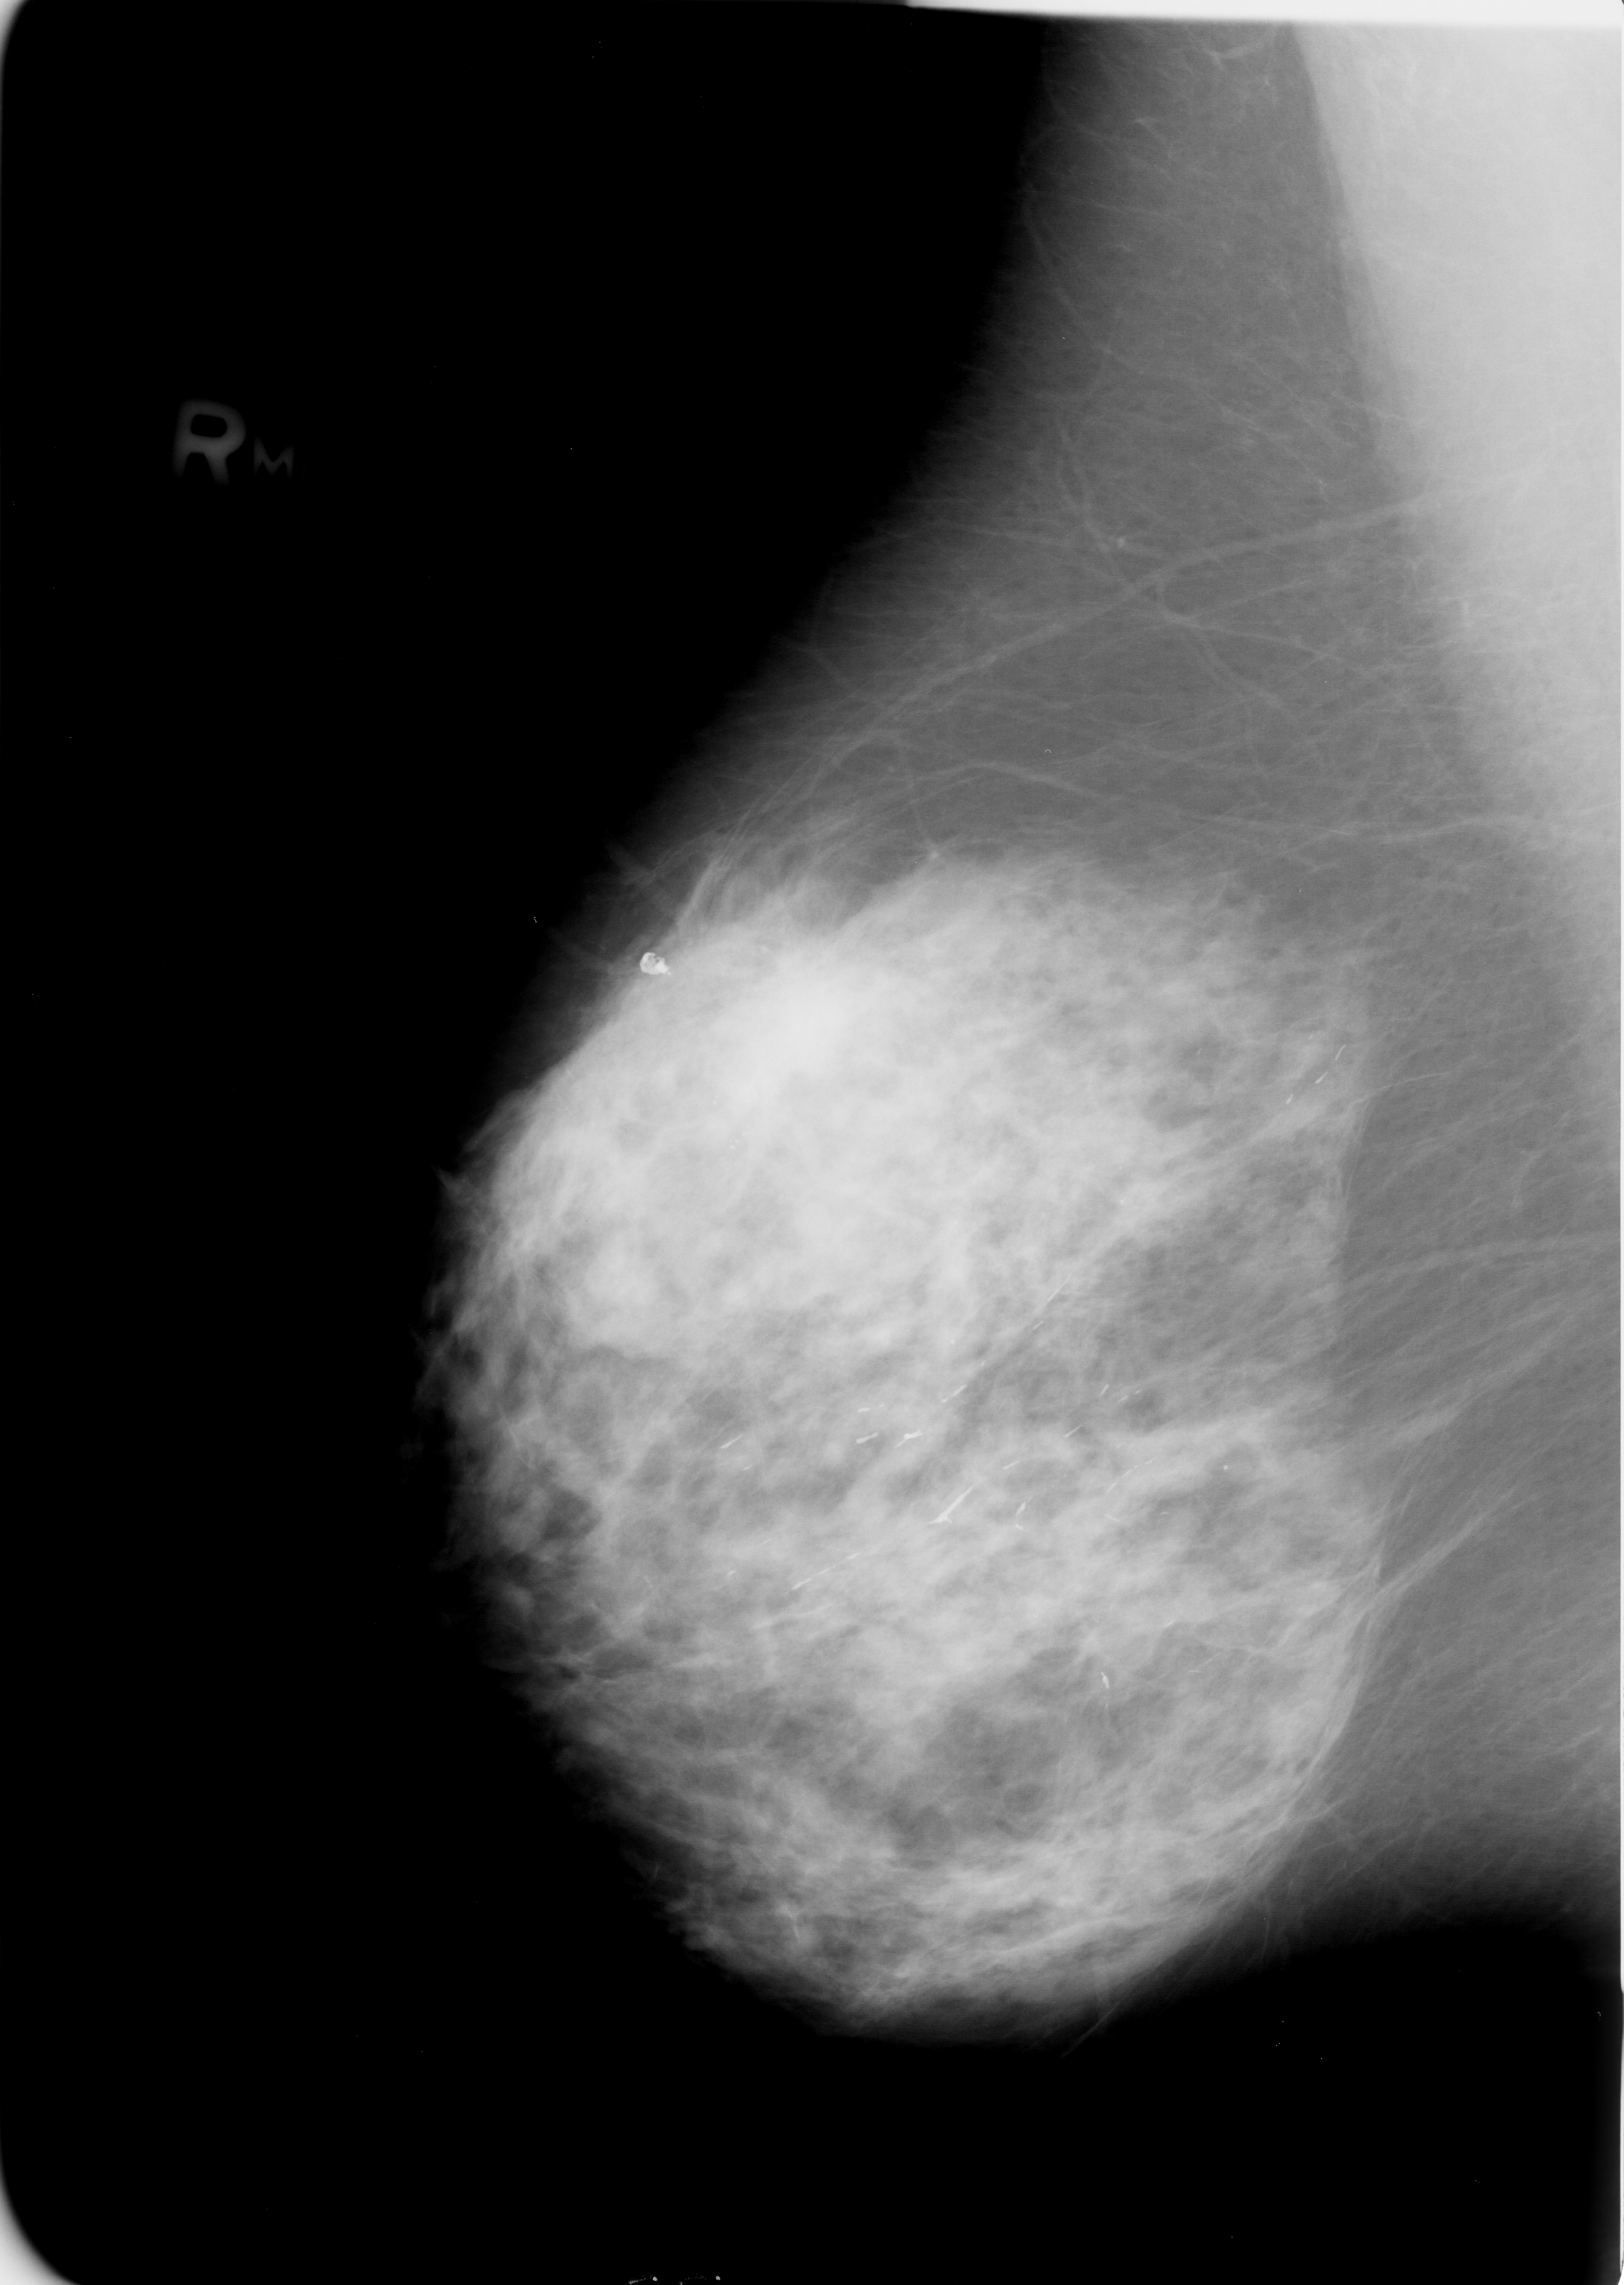
Scanned film-screen mammogram; right breast; MLO view; breast composition: heterogeneously dense (BI-RADS density category 3 of 4); 1624 × 2285 image matrix.
Expert-marked regions of interest on this image (one box per marked abnormality):
- Finding 1 of 3: calcifications, morphology pleomorphic, distribution clustered; BI-RADS assessment category 4; pathology (as recorded): malignant: box from (x=724, y=1088) to (x=747, y=1102) px
- Finding 2 of 3: calcifications, morphology pleomorphic, distribution clustered; BI-RADS assessment category 4; pathology result (as recorded, not read from the image): malignant: (x=743, y=1116)–(x=767, y=1134)
- Finding 3 of 3: calcifications, morphology pleomorphic, distribution clustered; BI-RADS assessment category 4; subtlety rating 3 on a 1 (subtle) to 5 (obvious) scale; pathology (as recorded): malignant: (x=765, y=1085)–(x=786, y=1102)